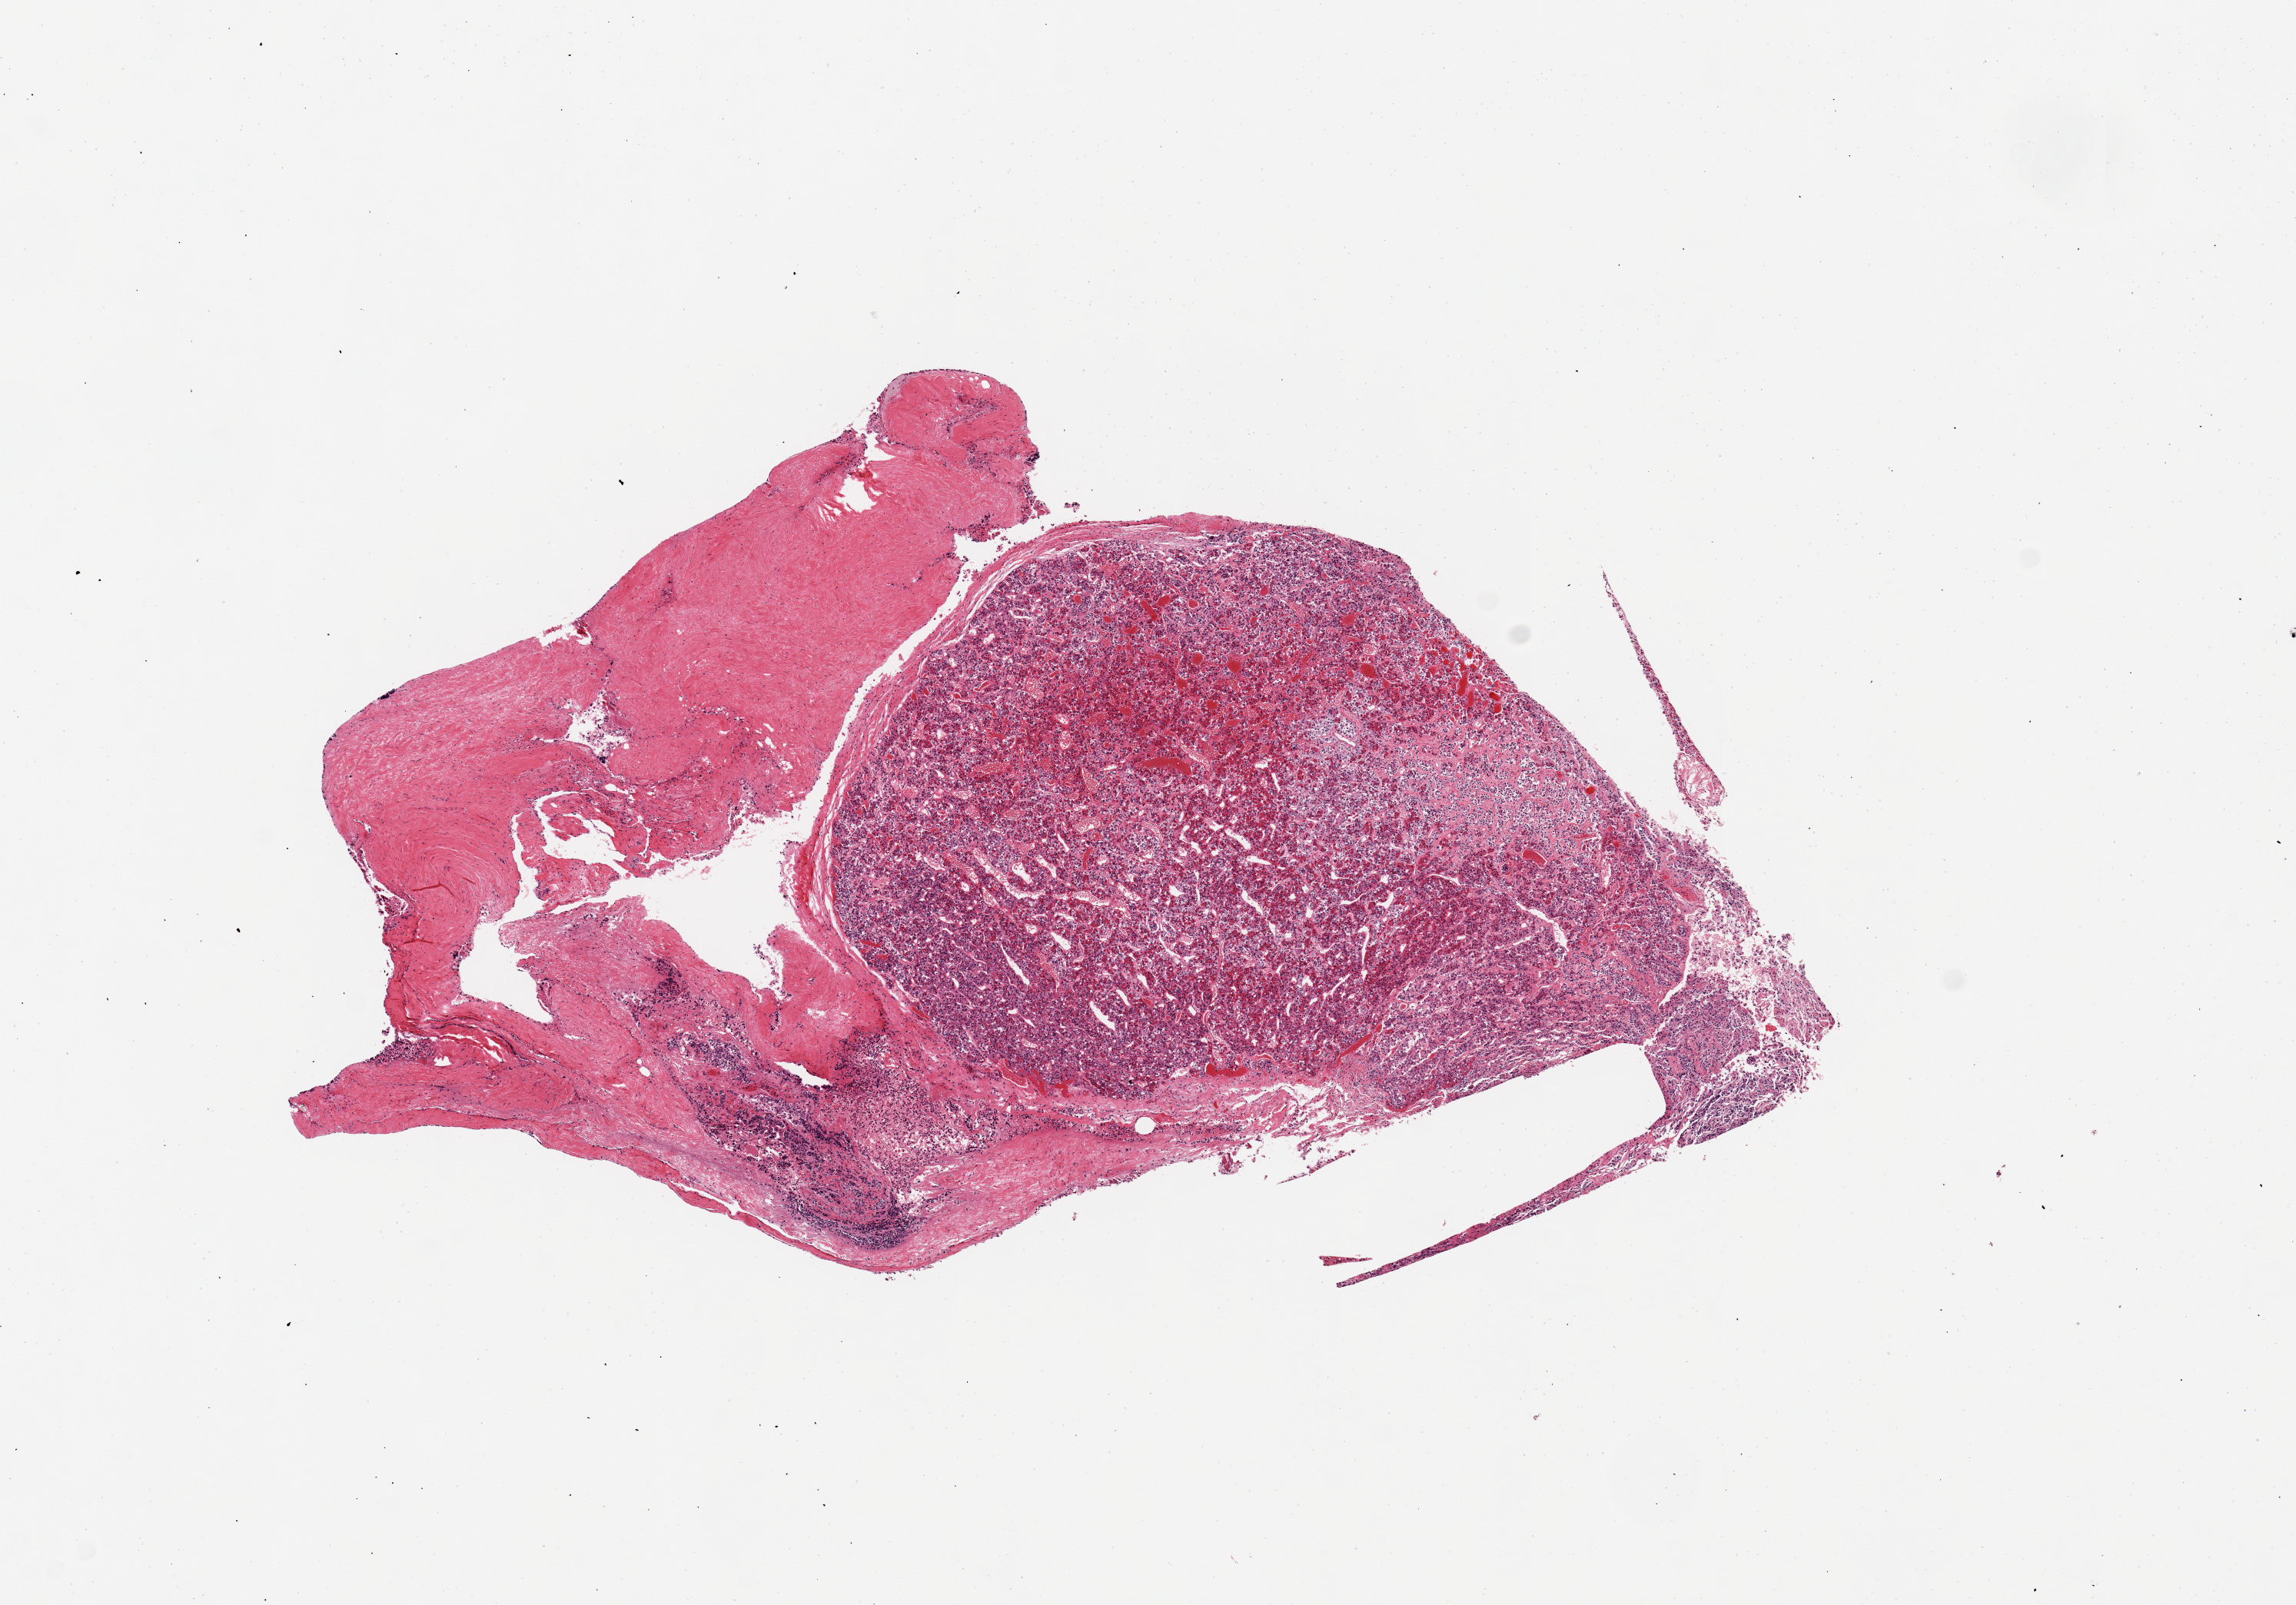
H&E whole-slide image, shown as a low-resolution overview of the whole scanned area (about 11.8 x 8.3 mm), PAXgene-fixed, paraffin-embedded tissue, section of pituitary (target tissue), donor tissue sample. Male donor.
- pathologist's review note for this sample: 1 piece; large amount [4x1 mm] of adherent dura